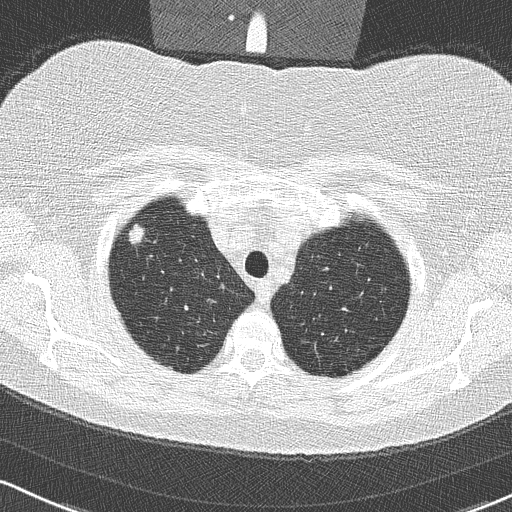
Low-dose screening chest CT, one axial slice. 120 kVp. Lung window (W 1500 / L -600 HU). 2 mm slice thickness. 512 × 512 image matrix, field of view 320 × 320 mm.
Outlined on this slice (expert manual segmentation):
- lesion 1 (tumor, upper lobe of right lung): box from (x=129, y=224) to (x=144, y=244) px